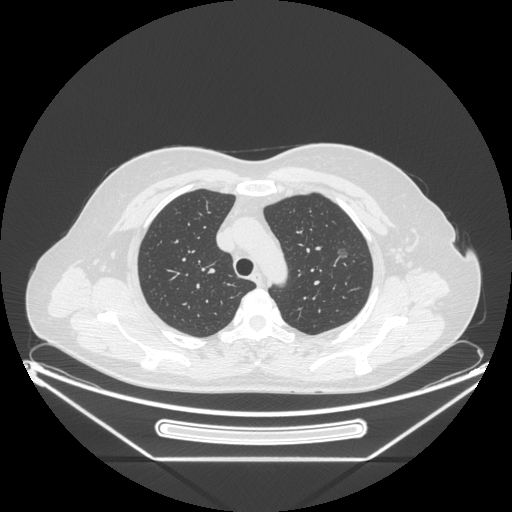
Chest CT, one axial slice. Slice 168 of 226 in the series (ordered by position). 120 kVp. Lung window (W 1500 / L -600 HU). 1.25 mm slice thickness. 512 × 512 image matrix, field of view 447 × 447 mm. Patient: female, 54 years. From the clinical record (not read from this slice): clinical TNM (as recorded): T1c N0 M0.
Outlined on this slice (rectangle marked by the reading radiologist):
- lung tumour (recorded histology: adenocarcinoma): bounding box <331,244,352,269> (left, top, right, bottom; pixels)